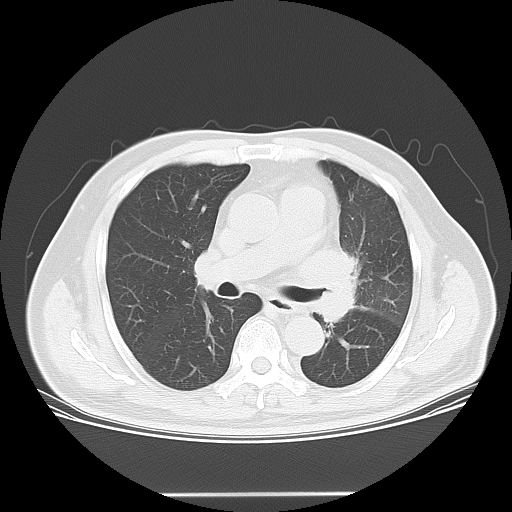
Chest CT, one axial slice; position 33 of 55 along the scan axis; reconstruction kernel LUNG; lung window (W 1500 / L -600 HU); 5 mm slice thickness; 512 × 512 image matrix, field of view 398 × 398 mm. Patient: male, 61 years. From the clinical record (not read from this slice): clinical TNM (as recorded): T3 N1 M1; histopathological grade: G3.
Structures marked on this image (rectangle marked by the reading radiologist):
- lung tumour (recorded histology: small cell carcinoma): bounding box (x1, y1, x2, y2) in pixels: (327, 239, 365, 330)